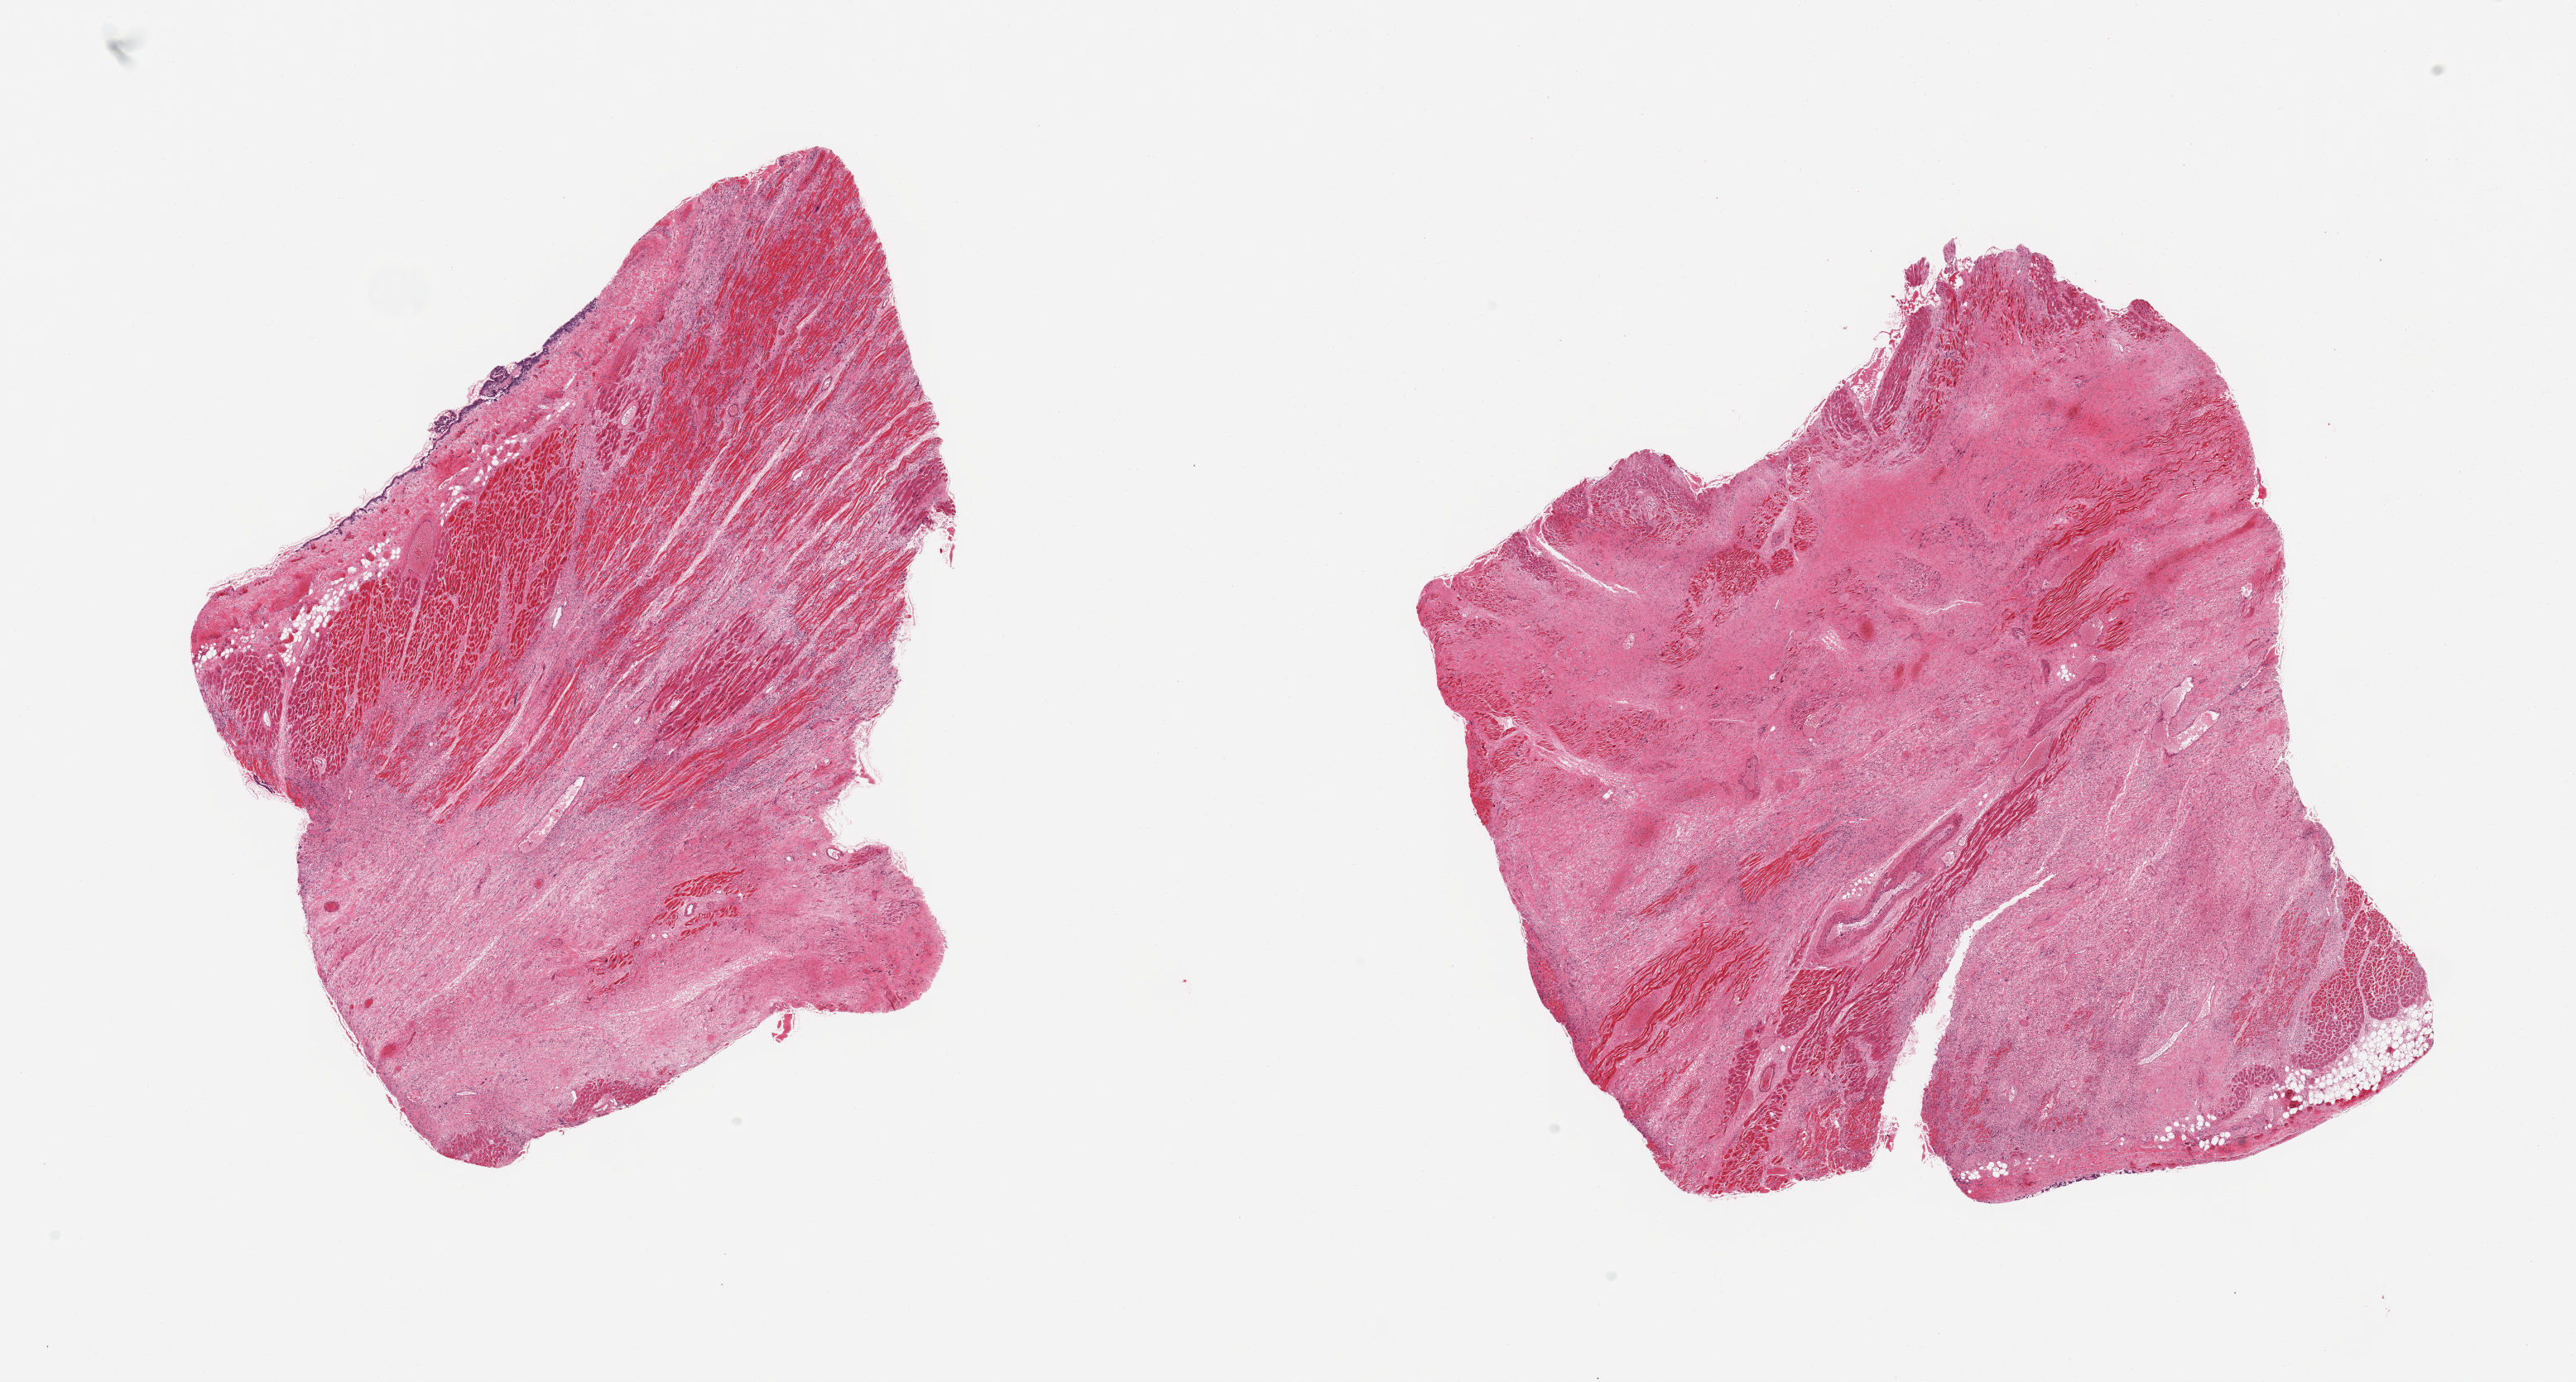
Digitized haematoxylin and eosin-stained section, brightfield, low-resolution overview of the scanned area, about 24.6 x 13.2 mm; PAXgene-fixed paraffin-embedded (PFPE) section; section of heart (target tissue); tissue donor sample. Donor: male.
Pathologist's review note for this sample: 2 pieces diffuse subacute myocardial infarct involves ~80% of aliquots.